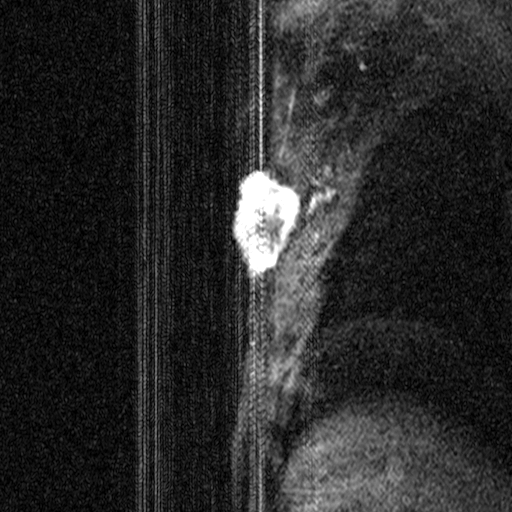
Breast MRI (dynamic contrast-enhanced), one sagittal slice. Position 30 of 44 along the scan axis. Dynamic contrast-enhanced study with each time point stored as its own series, time point 2 of 3 at this slice position (early post-contrast, ordered by acquisition time). 1.5 T. TE 4.5 ms, TR 11 ms. 3 mm slice thickness. 512 × 512 image matrix. Patient: female, 44 years. From the clinical record (not read from this slice): setting: breast cancer imaged before/during neoadjuvant chemotherapy; receptor status: HR-positive, HER2-negative.
Structures marked on this image (semi-automatically segmented with operator editing):
- analysis volume of interest (the breast-tissue region the enhancement analysis was run in; not a lesion): box from (x=206, y=164) to (x=305, y=299) px
- tumour enhancement mask (voxels above the 90 % enhancement threshold inside the analysis volume of interest): (x=234, y=167)–(x=299, y=269)